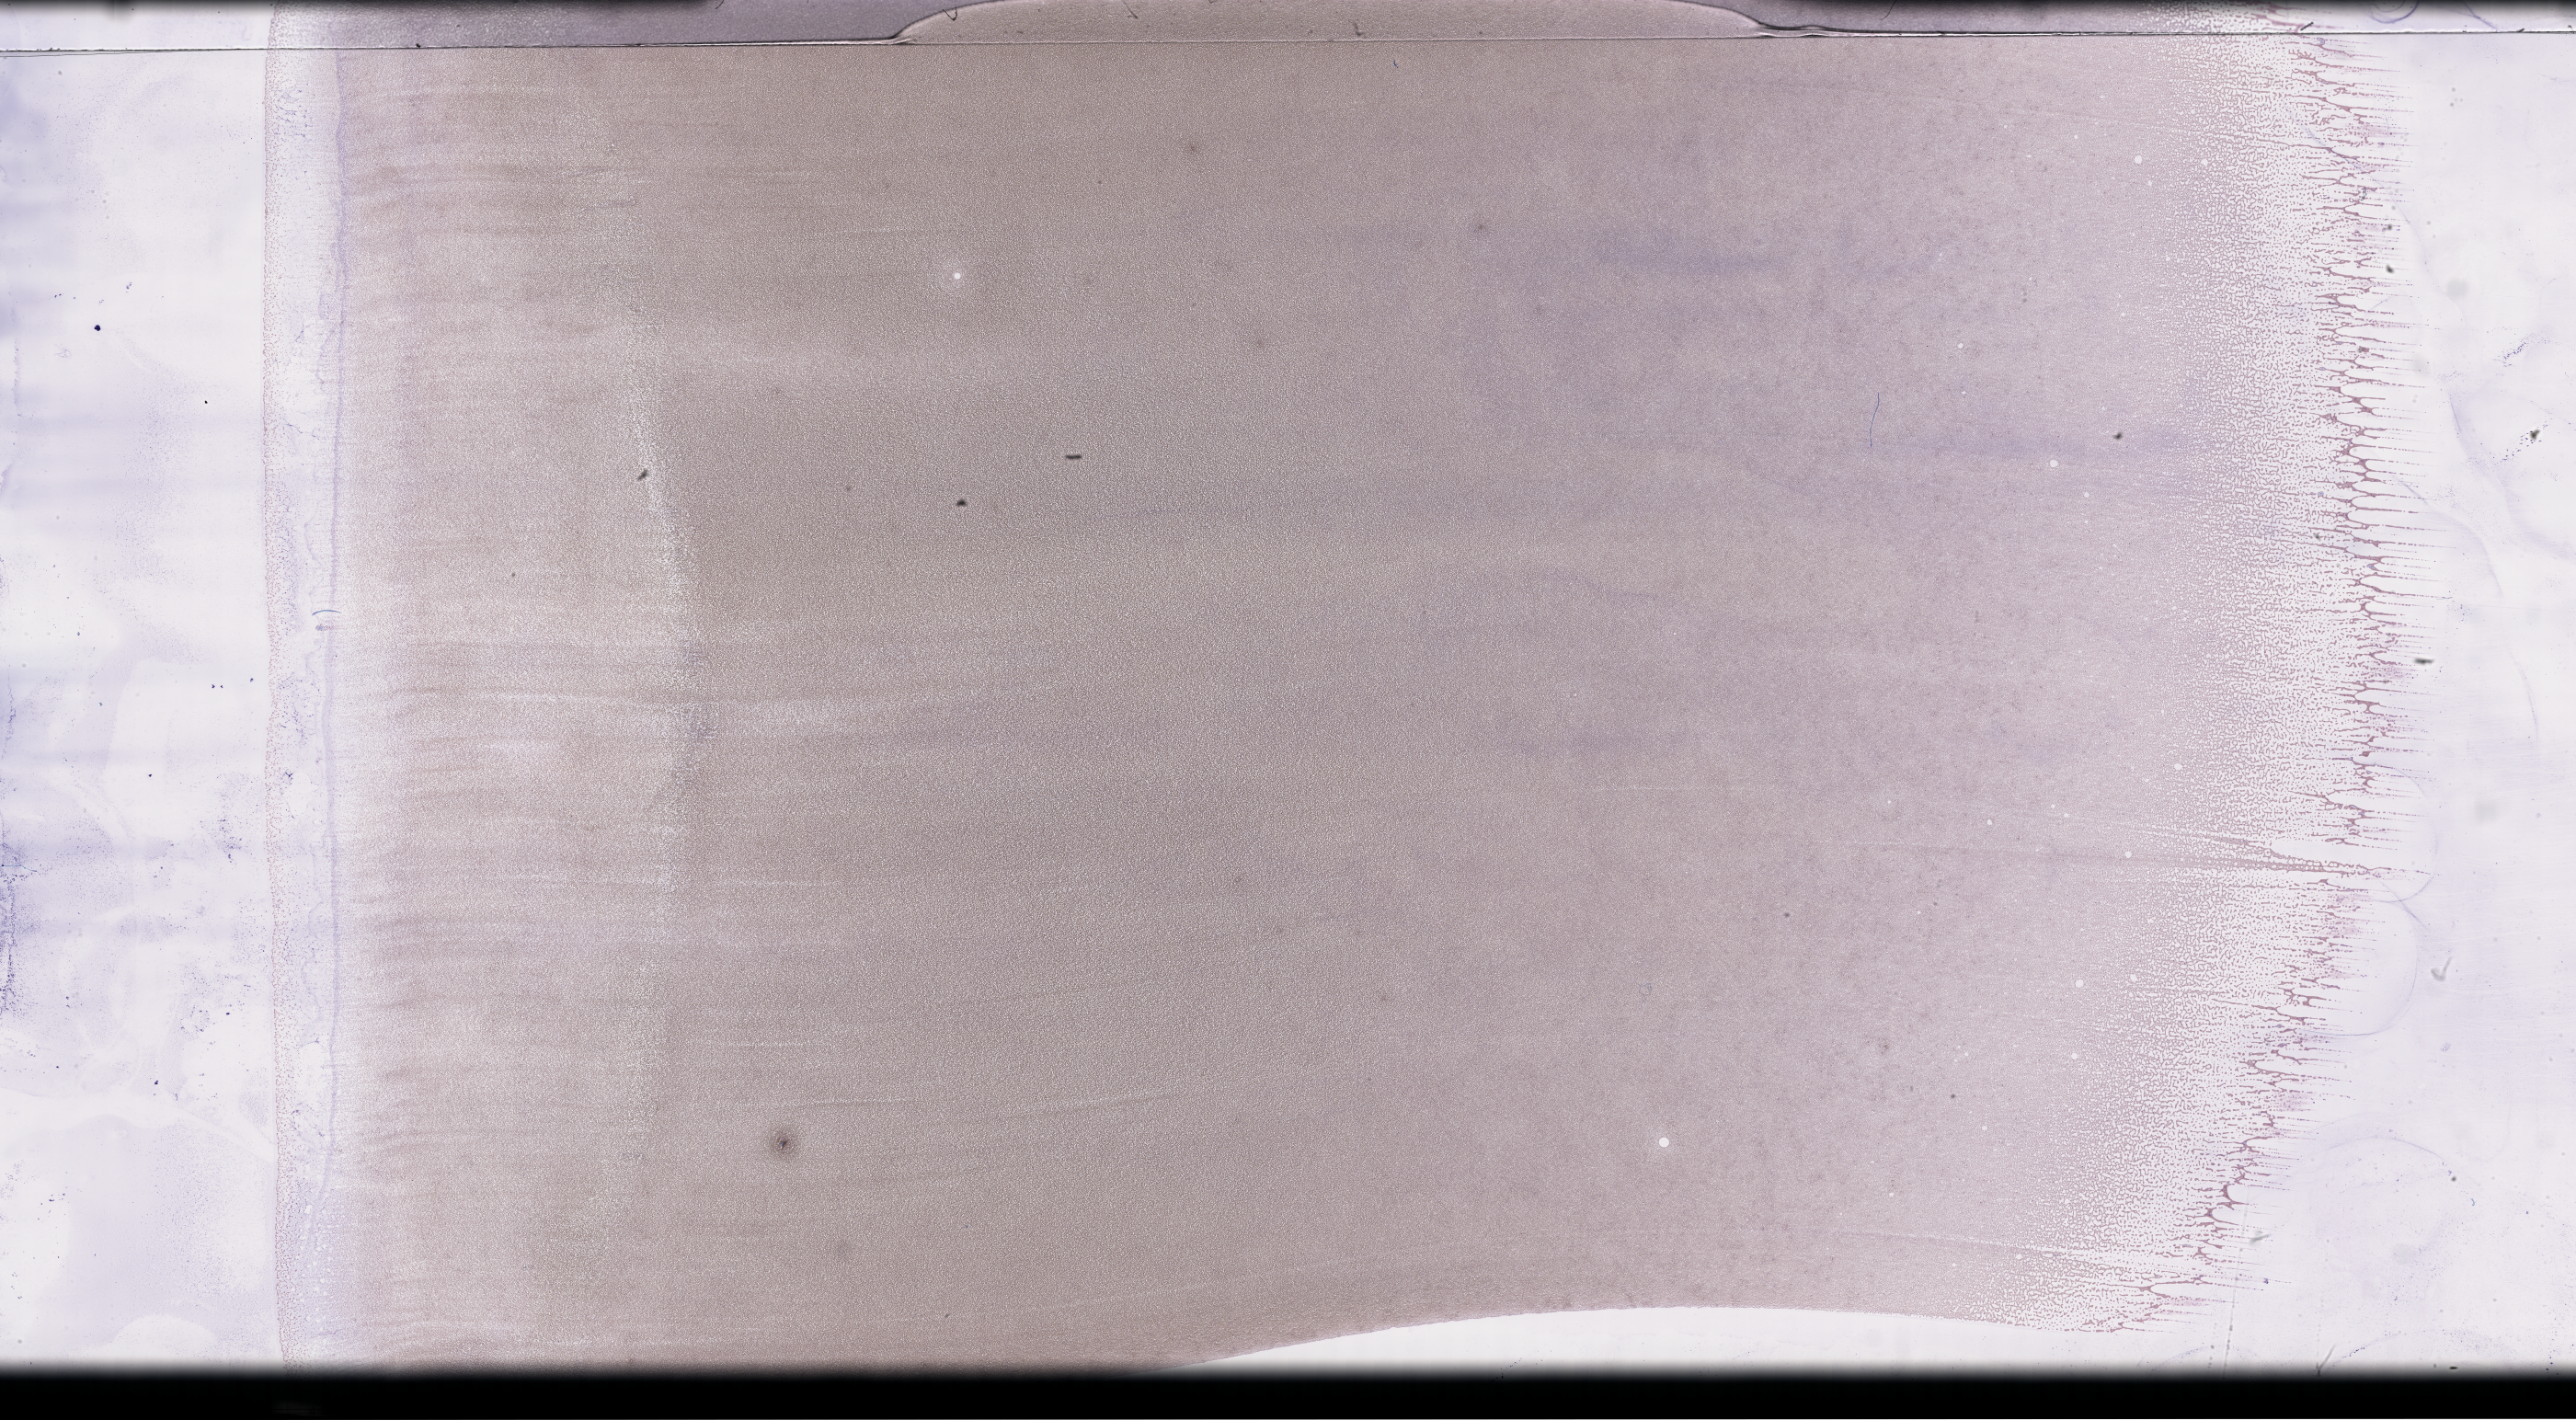
Whole-slide image of a whole blood smear, Wright–Giemsa stain — whole scanned area (about 45.2 x 24.9 mm) shown as a low-resolution overview. Patient: female.
Patient diagnosis: Plasma Cell Myeloma.